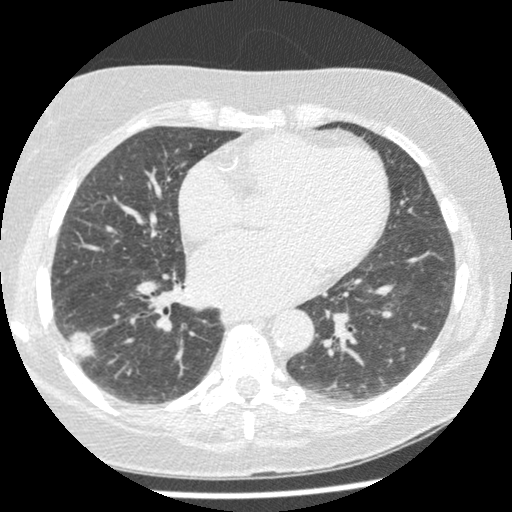
Low-dose screening chest CT, one axial slice; position 107 of 241 along the scan axis; 120 kVp; lung window (W 1500 / L -600 HU); 1.25 mm slice thickness; 512 × 512 image matrix.
Structures marked on this image (manually delineated by an expert):
- lesion 1 (tumor, lower lobe of right lung): bounding box <70,331,96,362> (left, top, right, bottom; pixels)